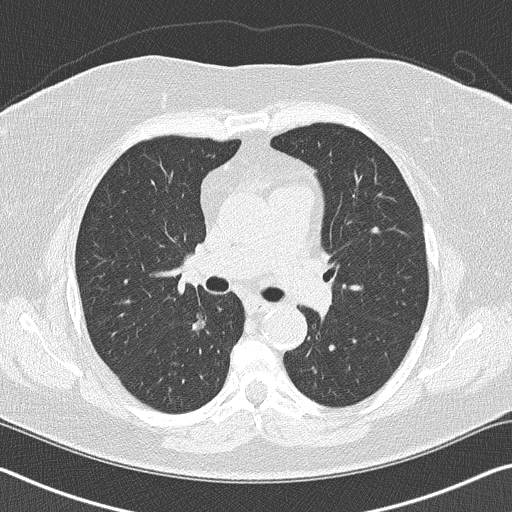
Chest CT (low-dose screening protocol), one axial image, baseline annual screen, lung window (W 1500 / L -600 HU). Female participant, aged 60 years at enrolment. Former smoker at enrolment.
- Expert reader's lesion annotation, box from (x=177, y=300) to (x=226, y=350) px.
- The screening reader recorded 2 non-calcified nodules or masses ≥4 mm on this exam; which of them this box marks is not recorded.
- Official screen result: positive, change unspecified: nodule(s) >= 4 mm or enlarging nodule(s), mass(es), or other non-specific abnormalities suspicious for lung cancer.
- Participant outcome: lung cancer diagnosed 482 days after this screen (after the second annual screen) — bronchiolo-alveolar carcinoma, non-mucinous, right lower lobe, stage IA (AJCC 6th edition), 15 mm at pathology.